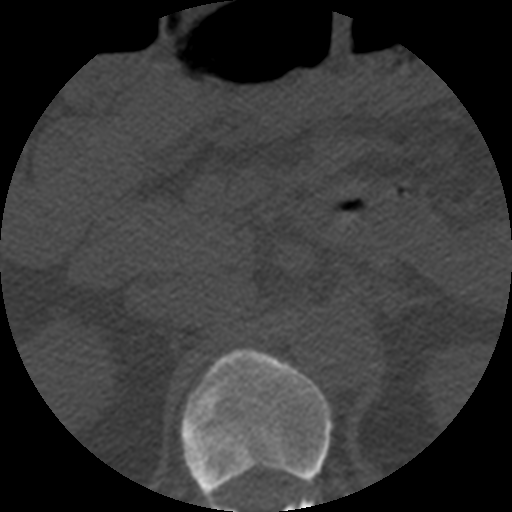
CT including the spine, one axial slice. Position 207 of 508 along the scan axis. Reconstruction kernel STANDARD. Bone window (W 1800 / L 400 HU). 1.25 mm slice thickness. 512 × 512 image matrix, field of view 160 × 160 mm. Patient age 57 years. From the clinical record (not read from this slice): primary cancer: prostate.
Outlined on this slice (semi-automatically segmented with operator editing):
- T12 vertebra: bounding box <180,350,333,512> (left, top, right, bottom; pixels)